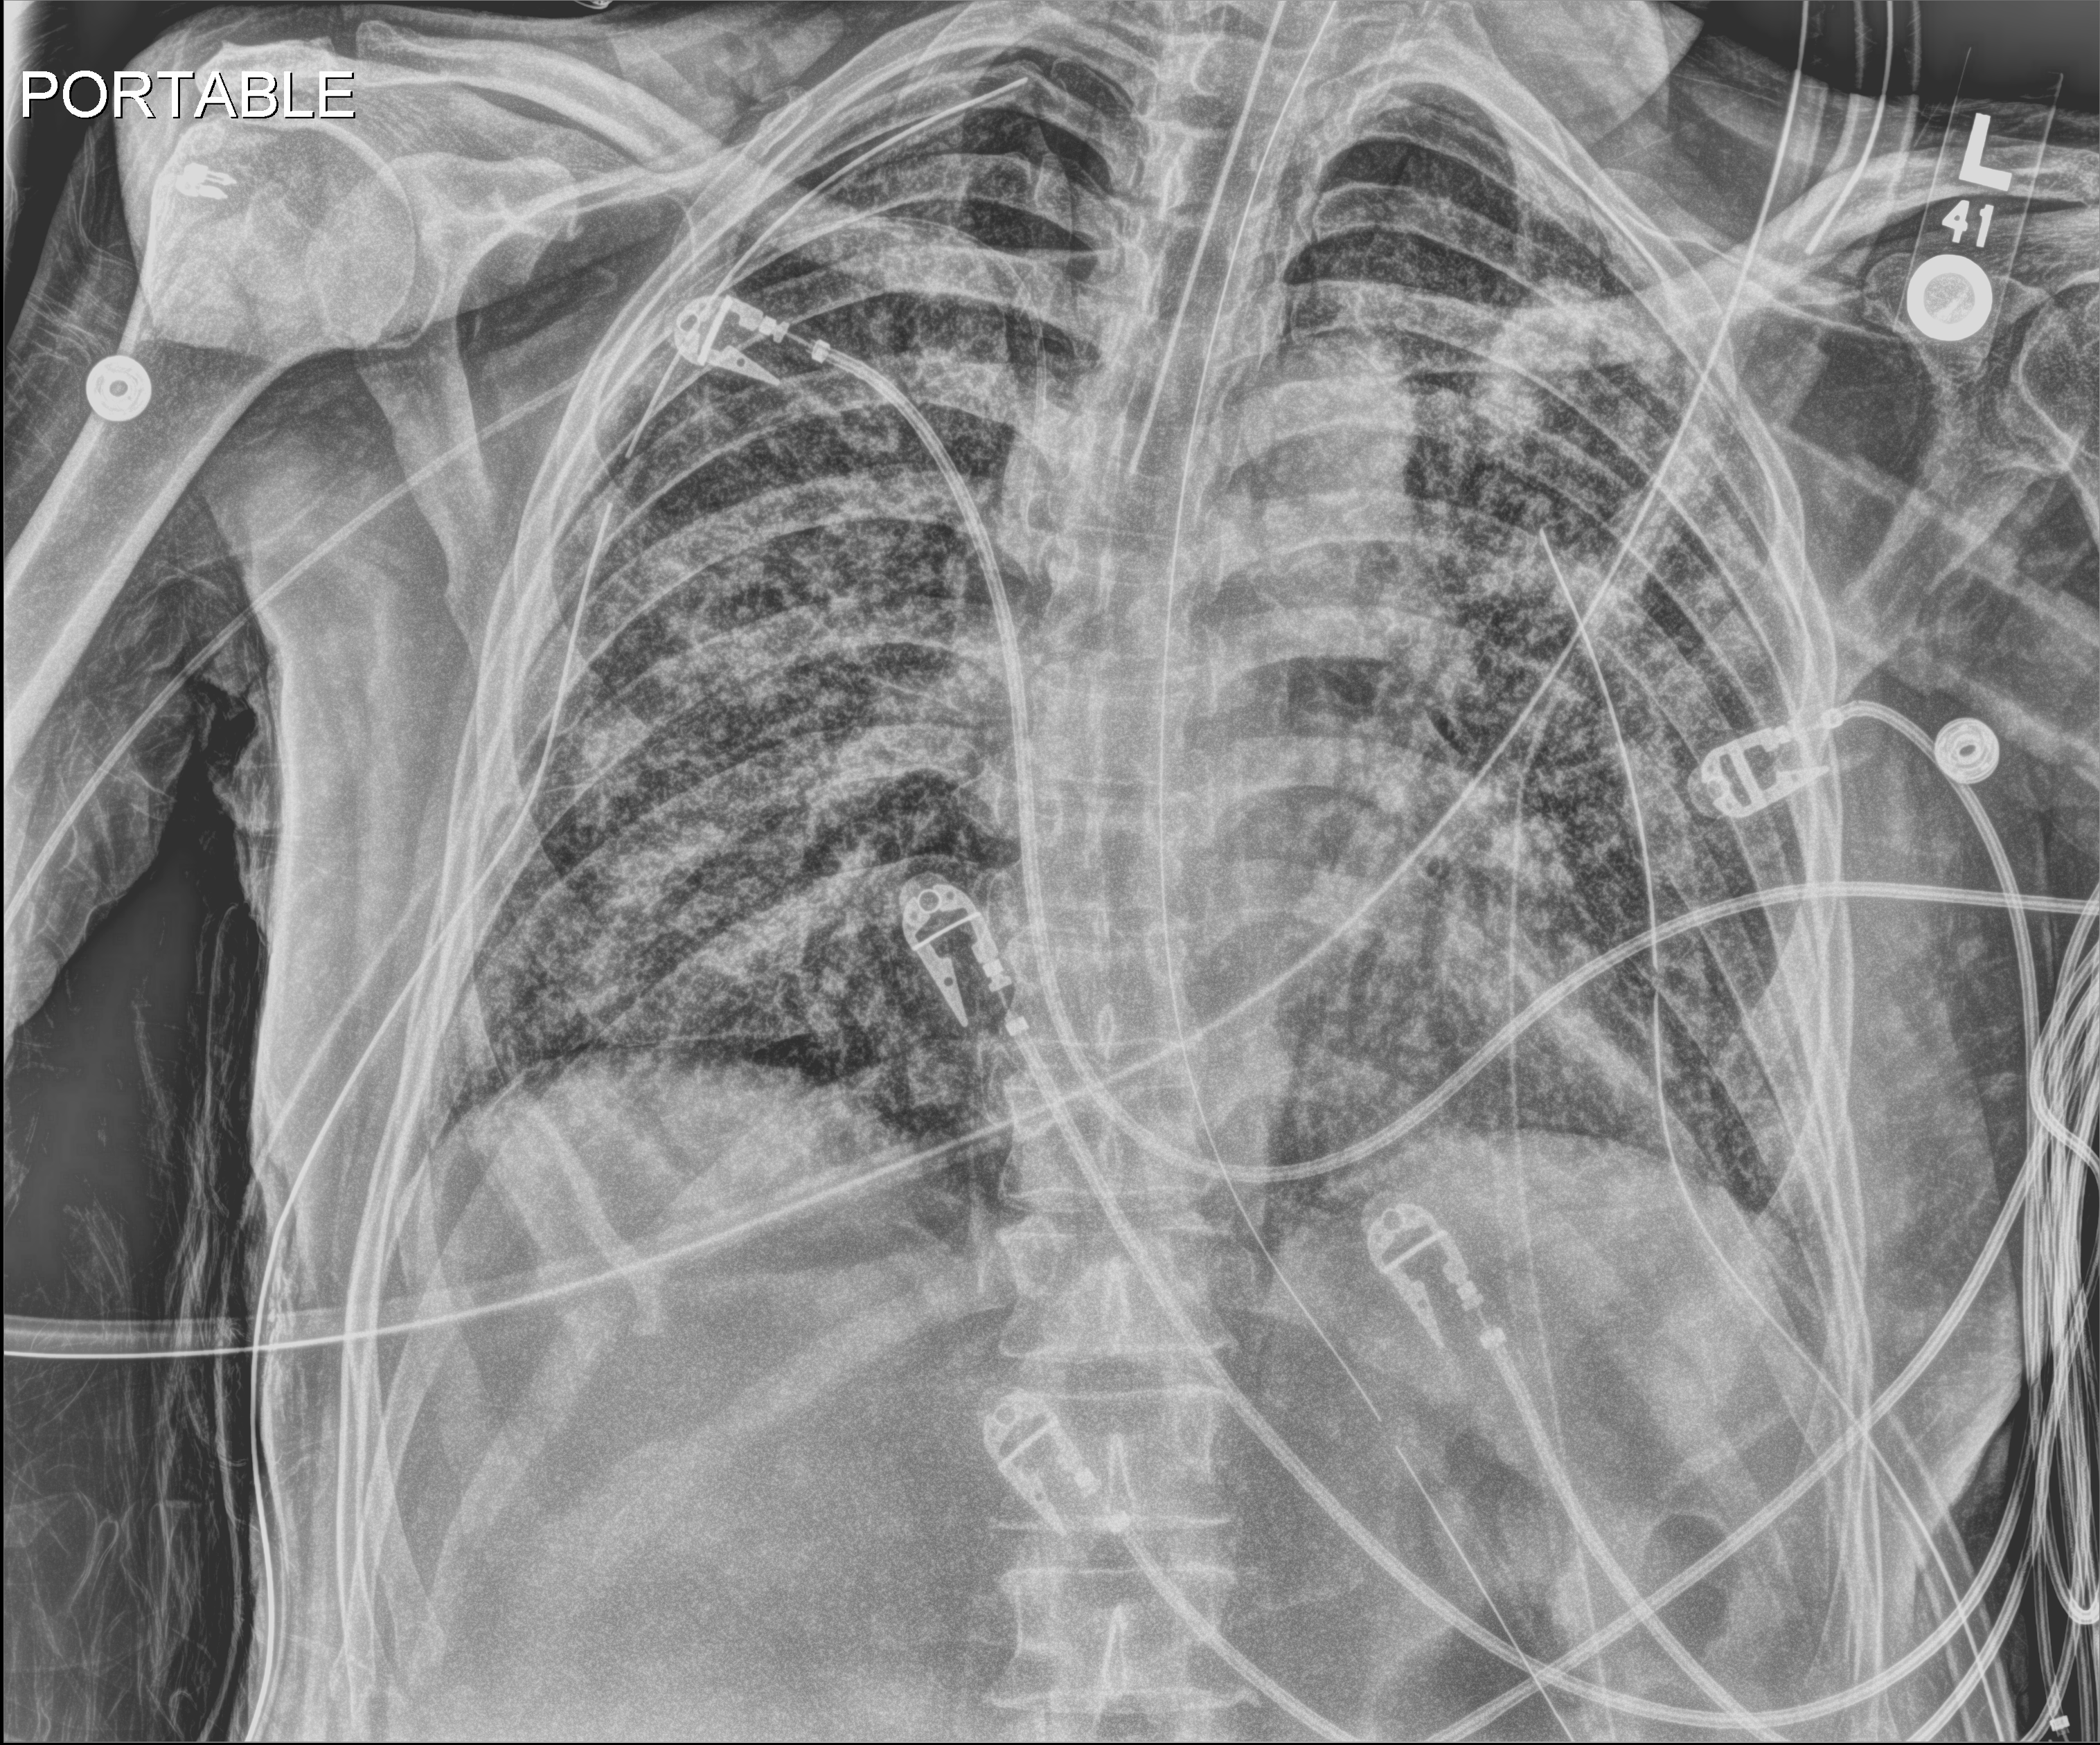
Bedside chest radiograph (digital radiography), anteroposterior (AP) projection. Patient hospitalised with COVID-19; male, aged 60–74 years.
Hospital-stay facts (about this admission, not read from this image; timing relative to this image not recorded): admitted to intensive care during this hospital stay: yes.